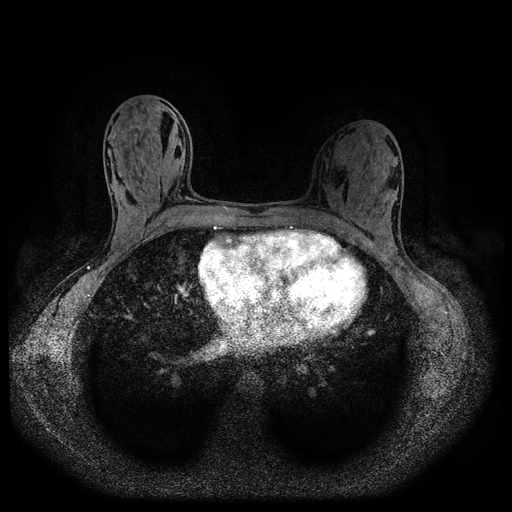
Breast MRI (dynamic contrast-enhanced, multi-phase), one axial slice; slice 49 of 116 in the series (ordered by position); dynamic contrast-enhanced series, time point 2 of 5 at this slice position (early post-contrast); 1.5 T; TE 2.7 ms, TR 5.4 ms; 2 mm slice thickness; 512 × 512 image matrix. Female patient, age 32 years.
Outlined on this slice (semi-automatically segmented with operator editing):
- breast lesion (labelled benign in the annotation): bounding box [x1, y1, x2, y2] px = [132, 113, 142, 123]